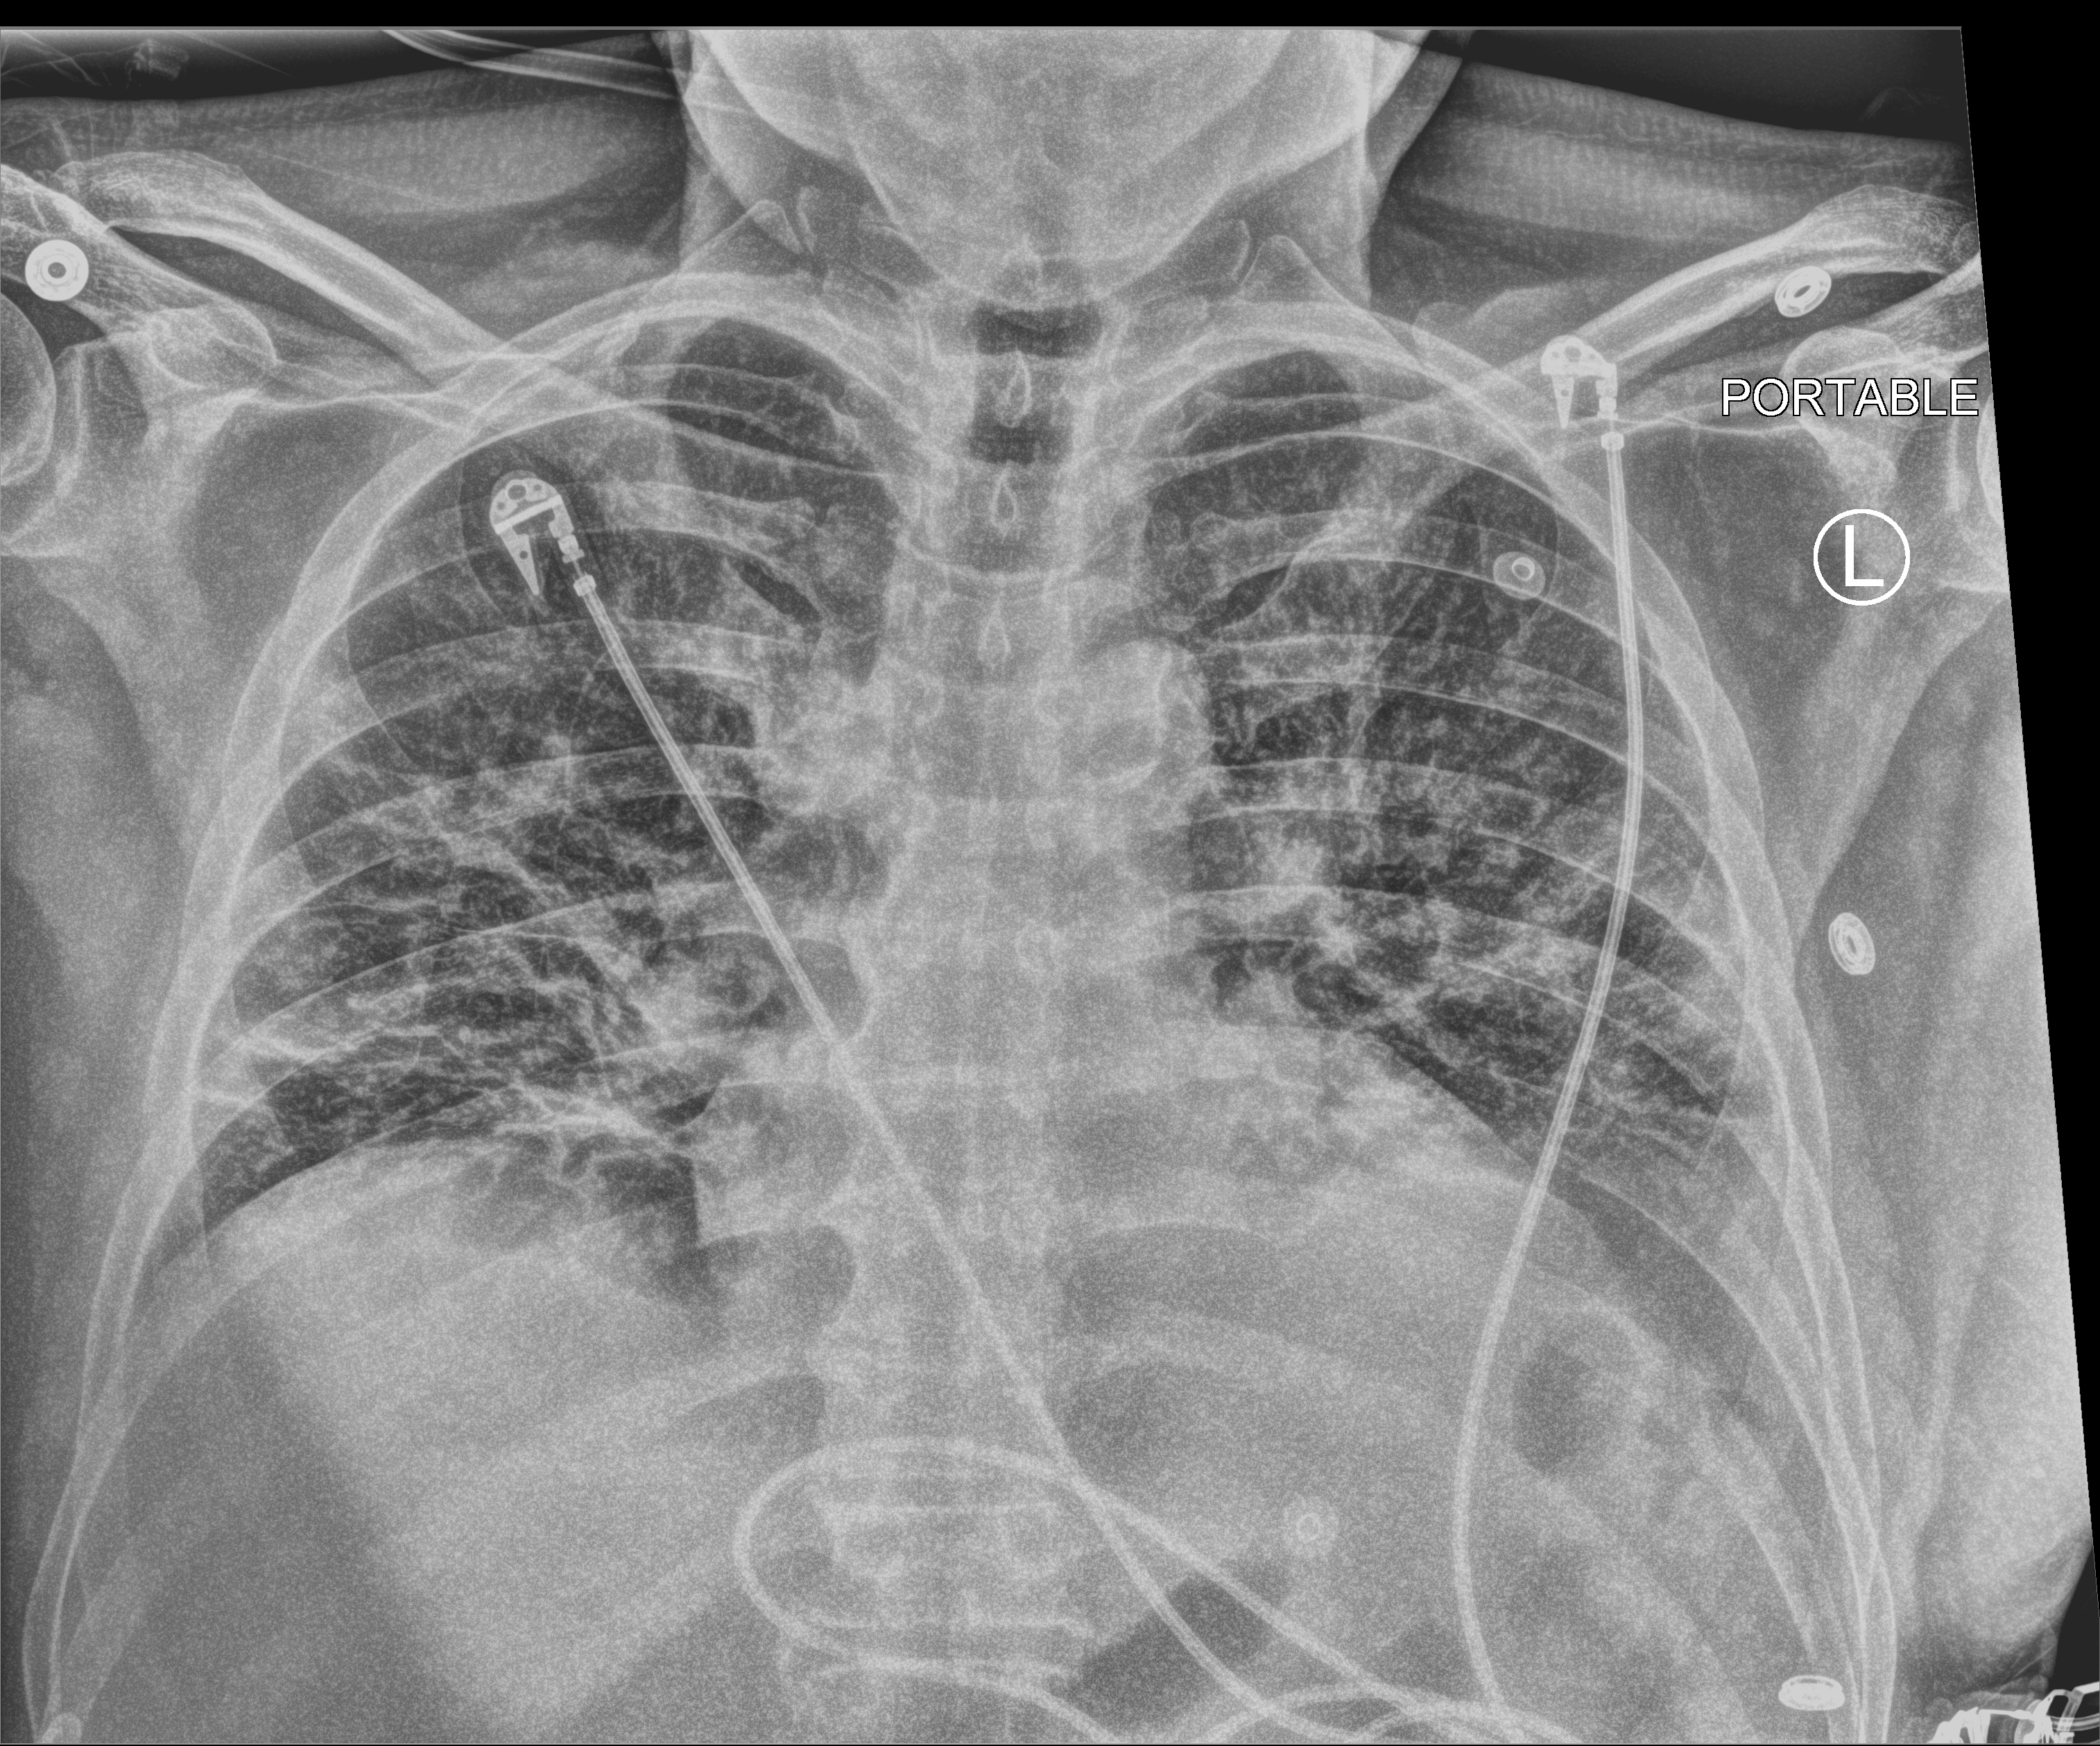
Portable chest radiograph. Male patient hospitalised with COVID-19, age 60–74 years.
Admission-level facts for this patient (not findings on this image; timing relative to this image not recorded): mechanically ventilated during this hospital stay: no; admitted to intensive care during this hospital stay: no.